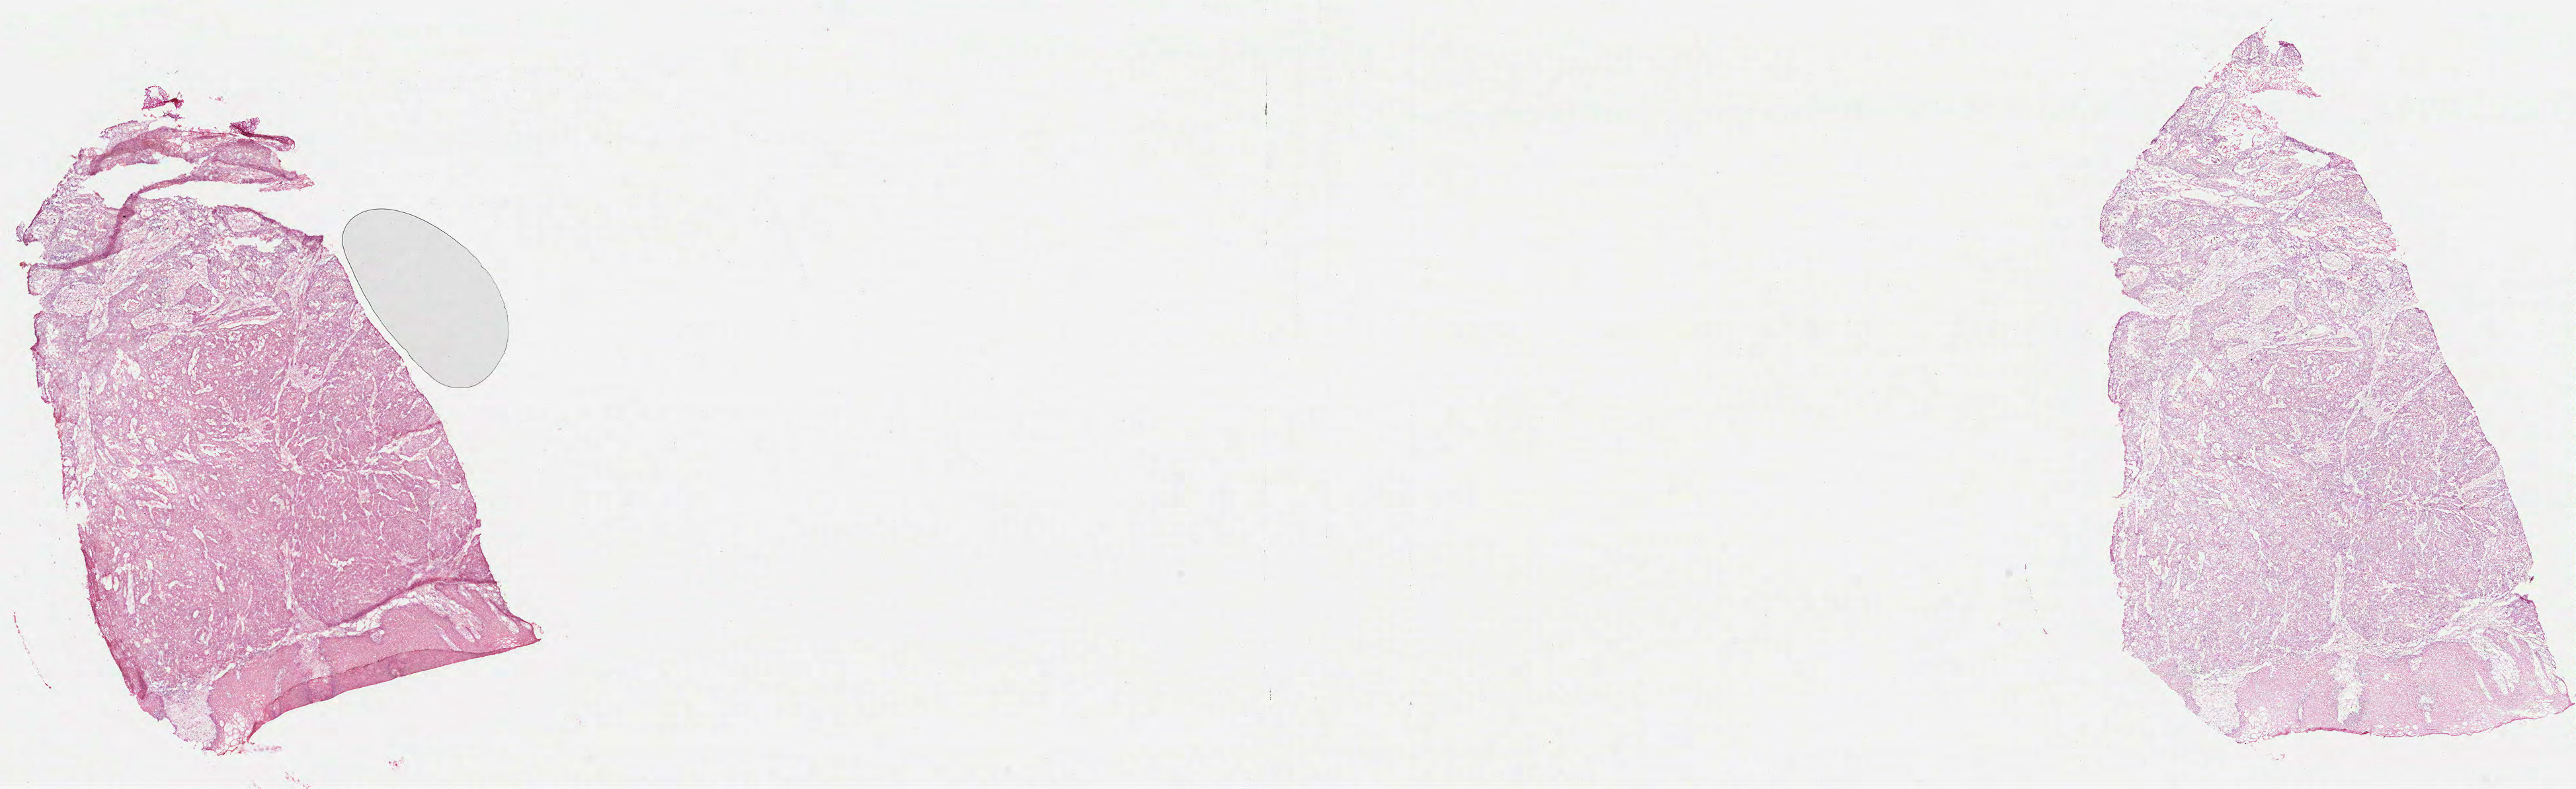
Digitized H&E-stained tissue section (whole slide), whole scanned area (about 31.4 x 9.6 mm) shown as a low-resolution overview. Formalin-fixed paraffin-embedded (FFPE) diagnostic section. Primary tumour sample from the head and neck. Male patient; age at initial diagnosis 52 years. Histologic grade: G2 (moderately differentiated).
Pathologic diagnosis: Squamous cell carcinoma, NOS (tongue, NOS). AJCC pathologic stage: IVA (7th edition).